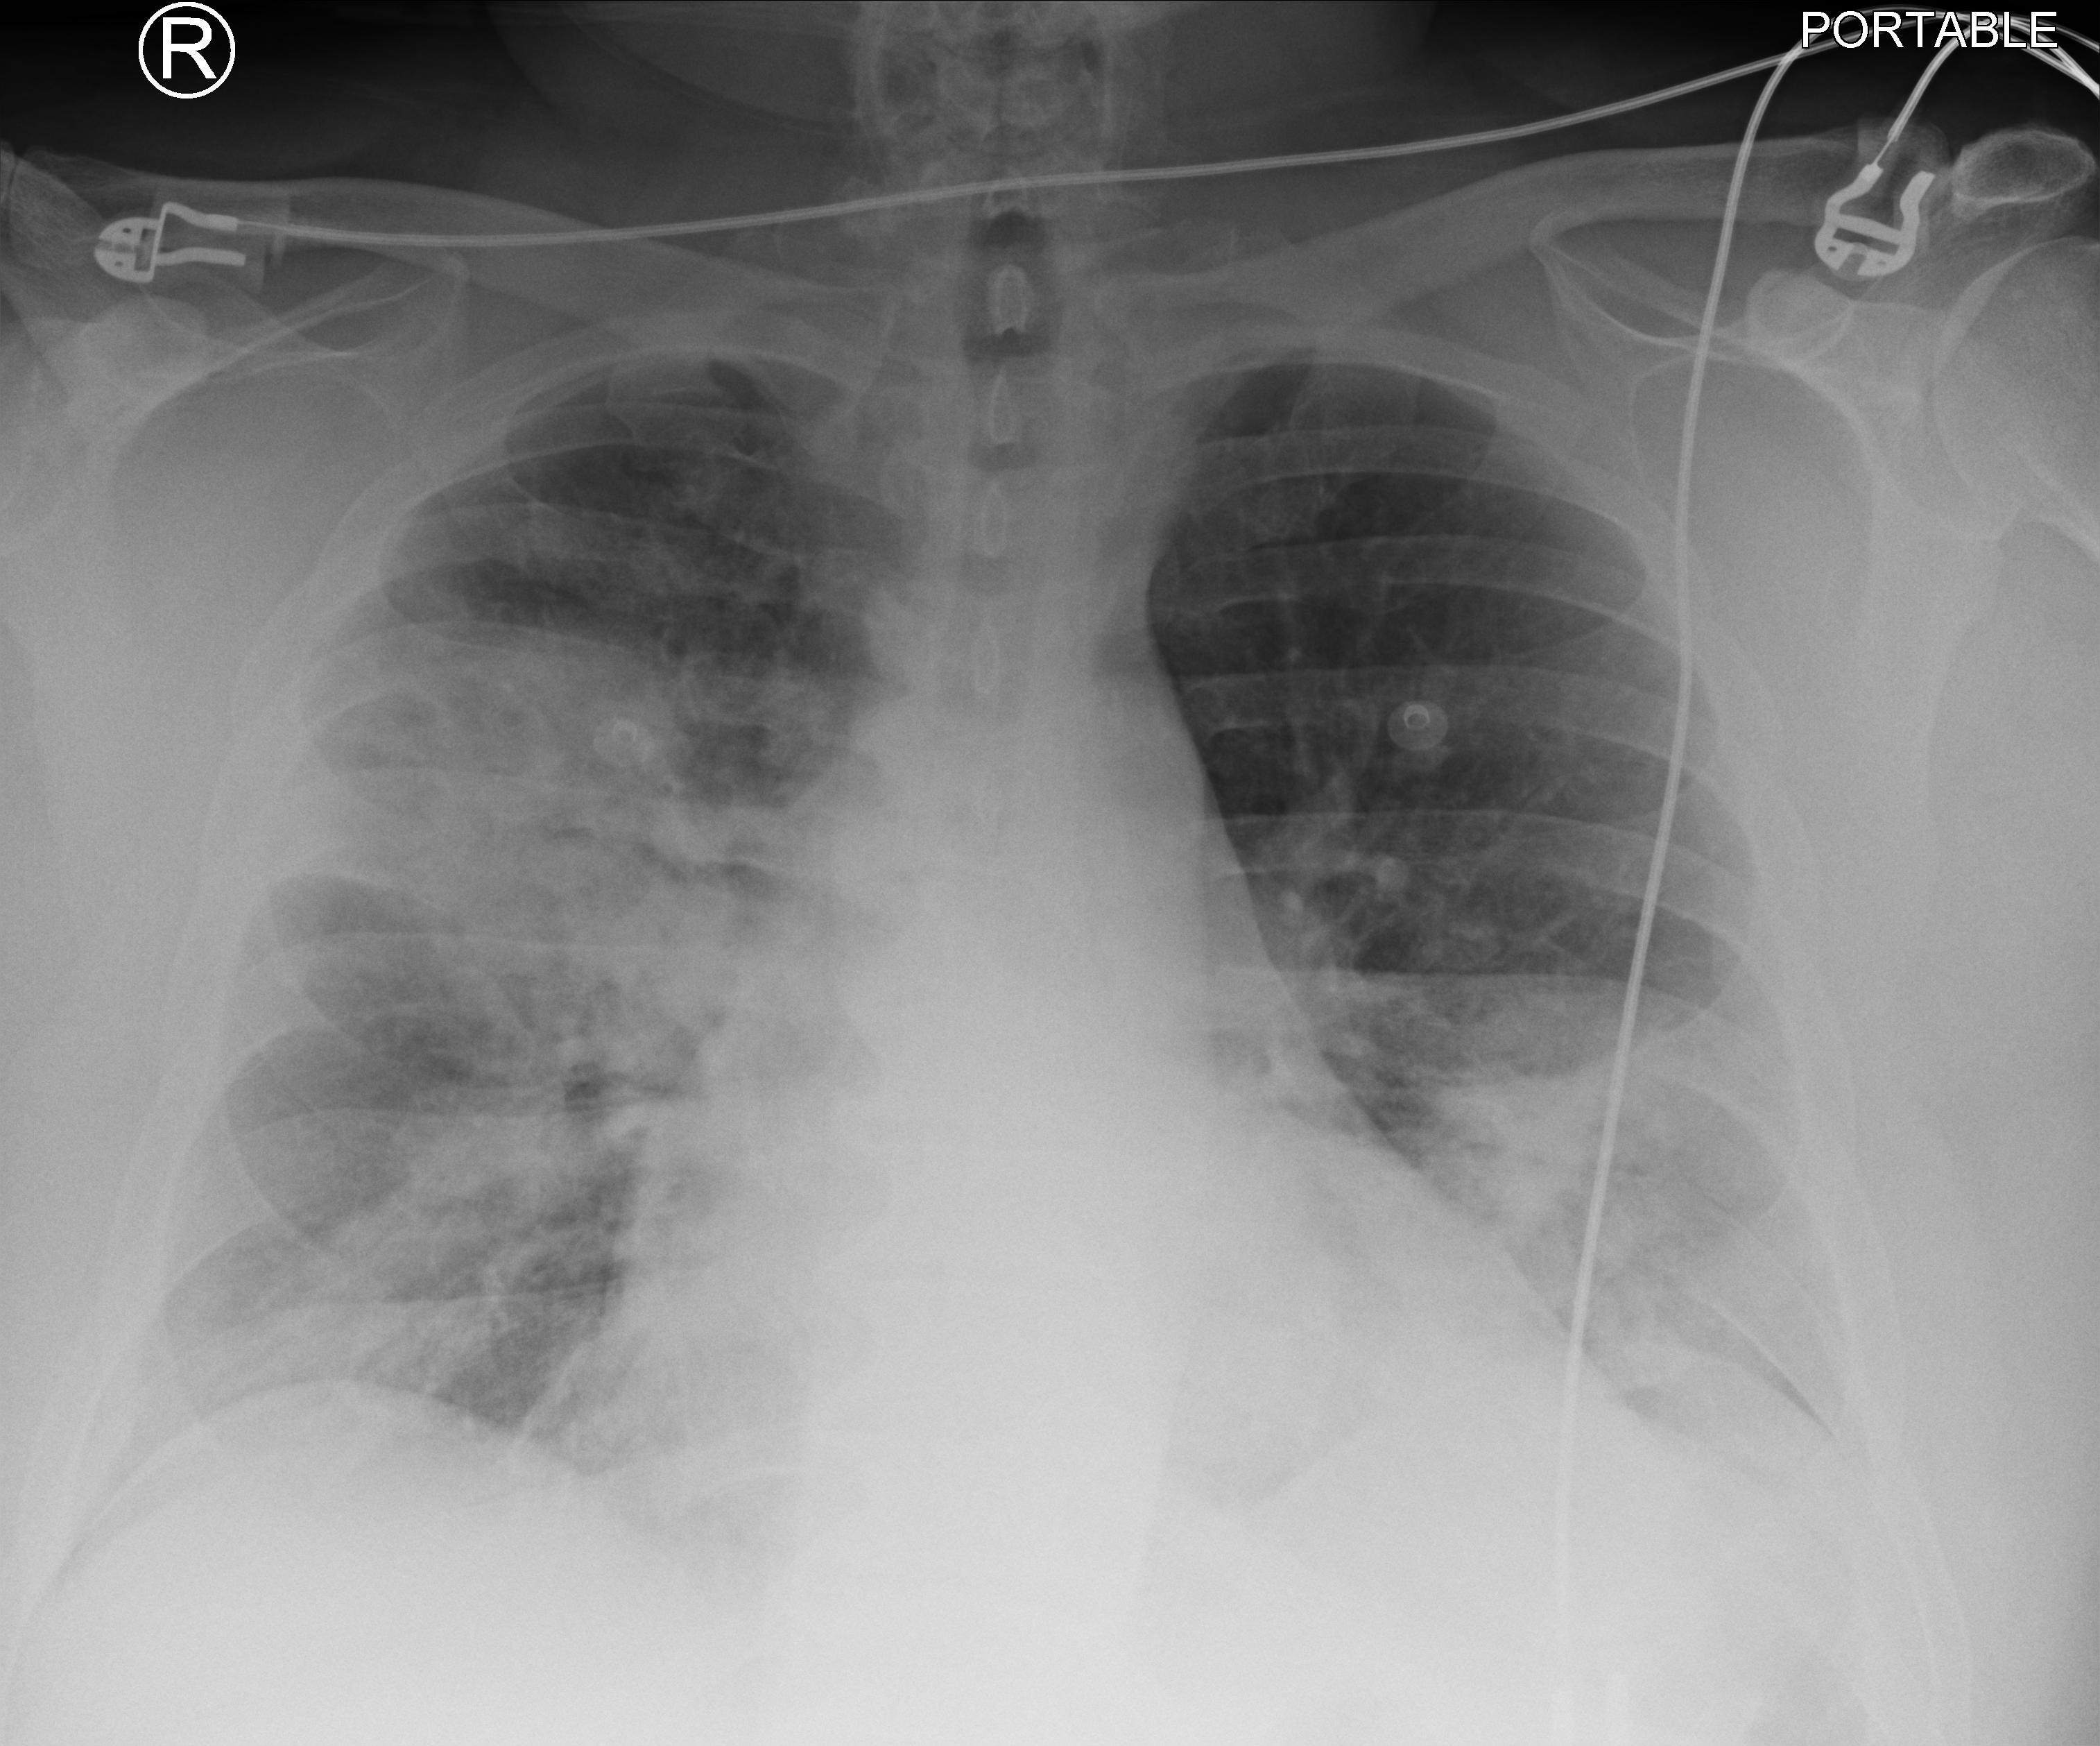
Portable chest radiograph; anteroposterior (AP) projection. Male patient hospitalised with COVID-19, age 18–59 years.
From the hospital-stay record, not from the radiograph (when in the stay this image was taken is not recorded): length of hospital stay: 9 days; admitted to intensive care during this hospital stay: no; smoking status (admission record): current.